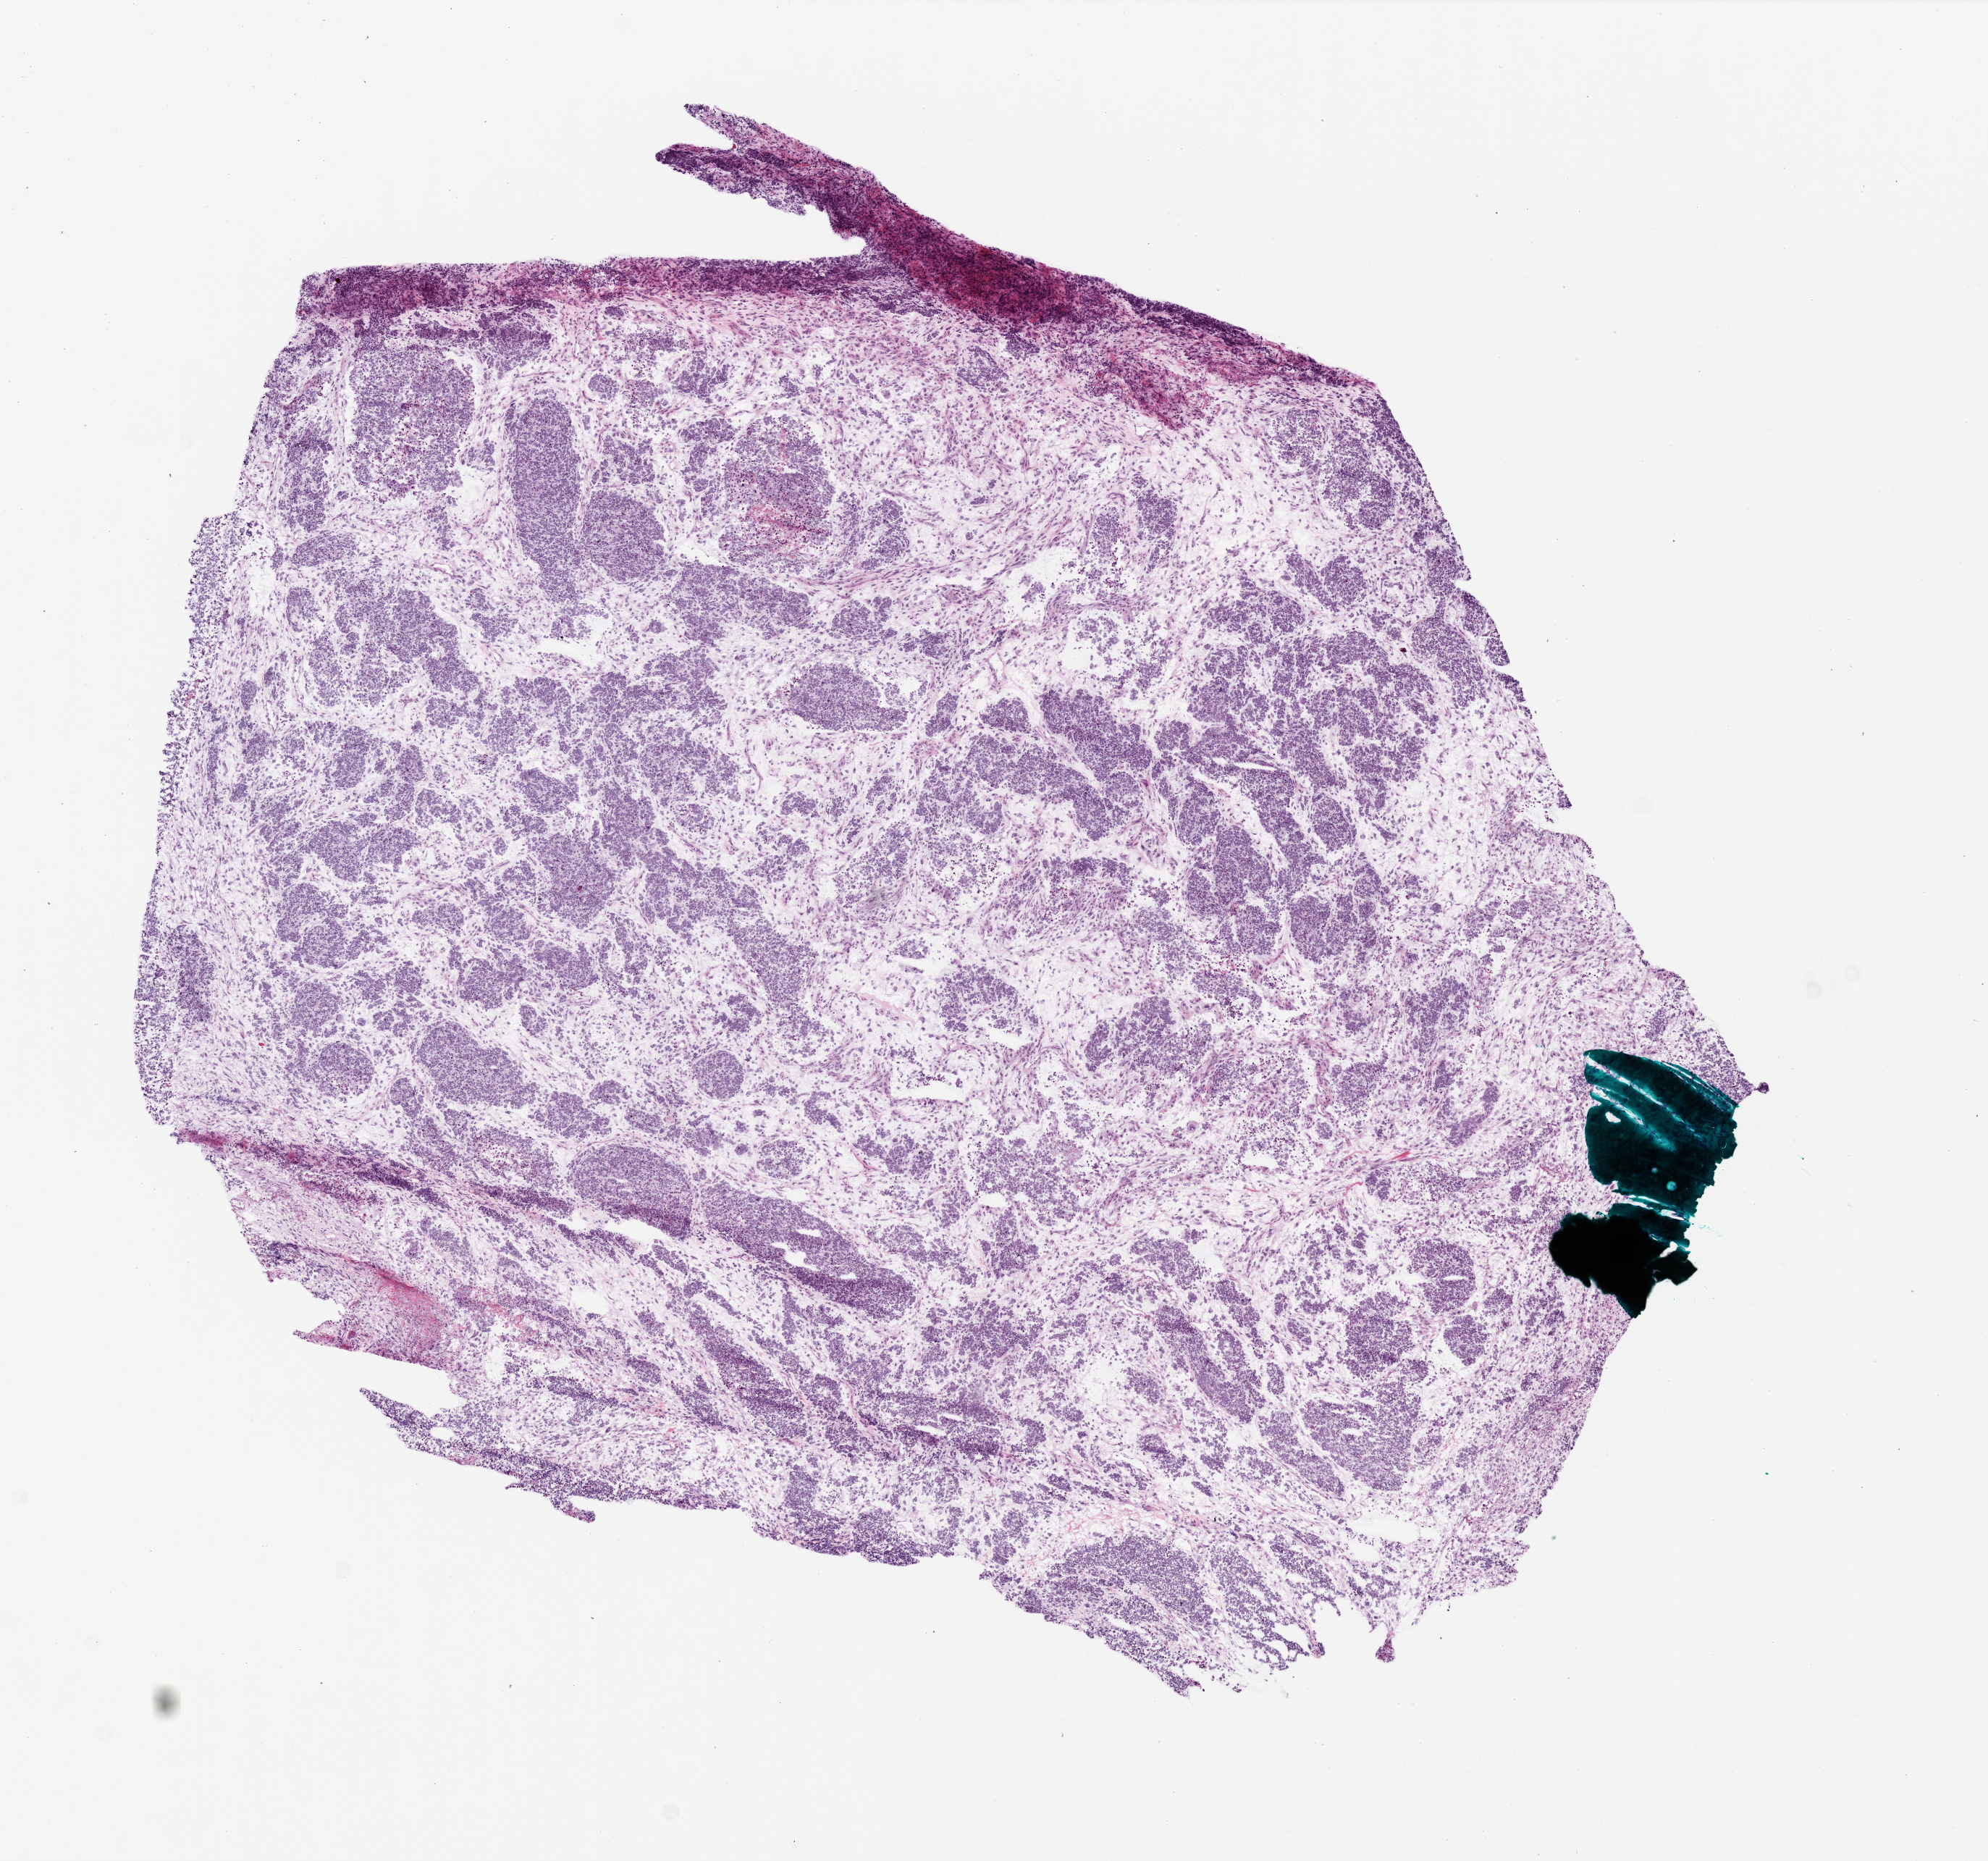
Hematoxylin and eosin (H&E) stained whole-slide image, low-resolution overview of the scanned area, about 11.0 x 10.3 mm (acquisition: 20x scan), frozen section, brain, primary tumour sample. Patient: male, age at initial diagnosis 75 years. Slide review estimates, as recorded: tumour cells 85%, tumour nuclei 90%, normal cells 0%, stromal cells 15%, necrosis 0%.
• pathologic diagnosis: Glioblastoma